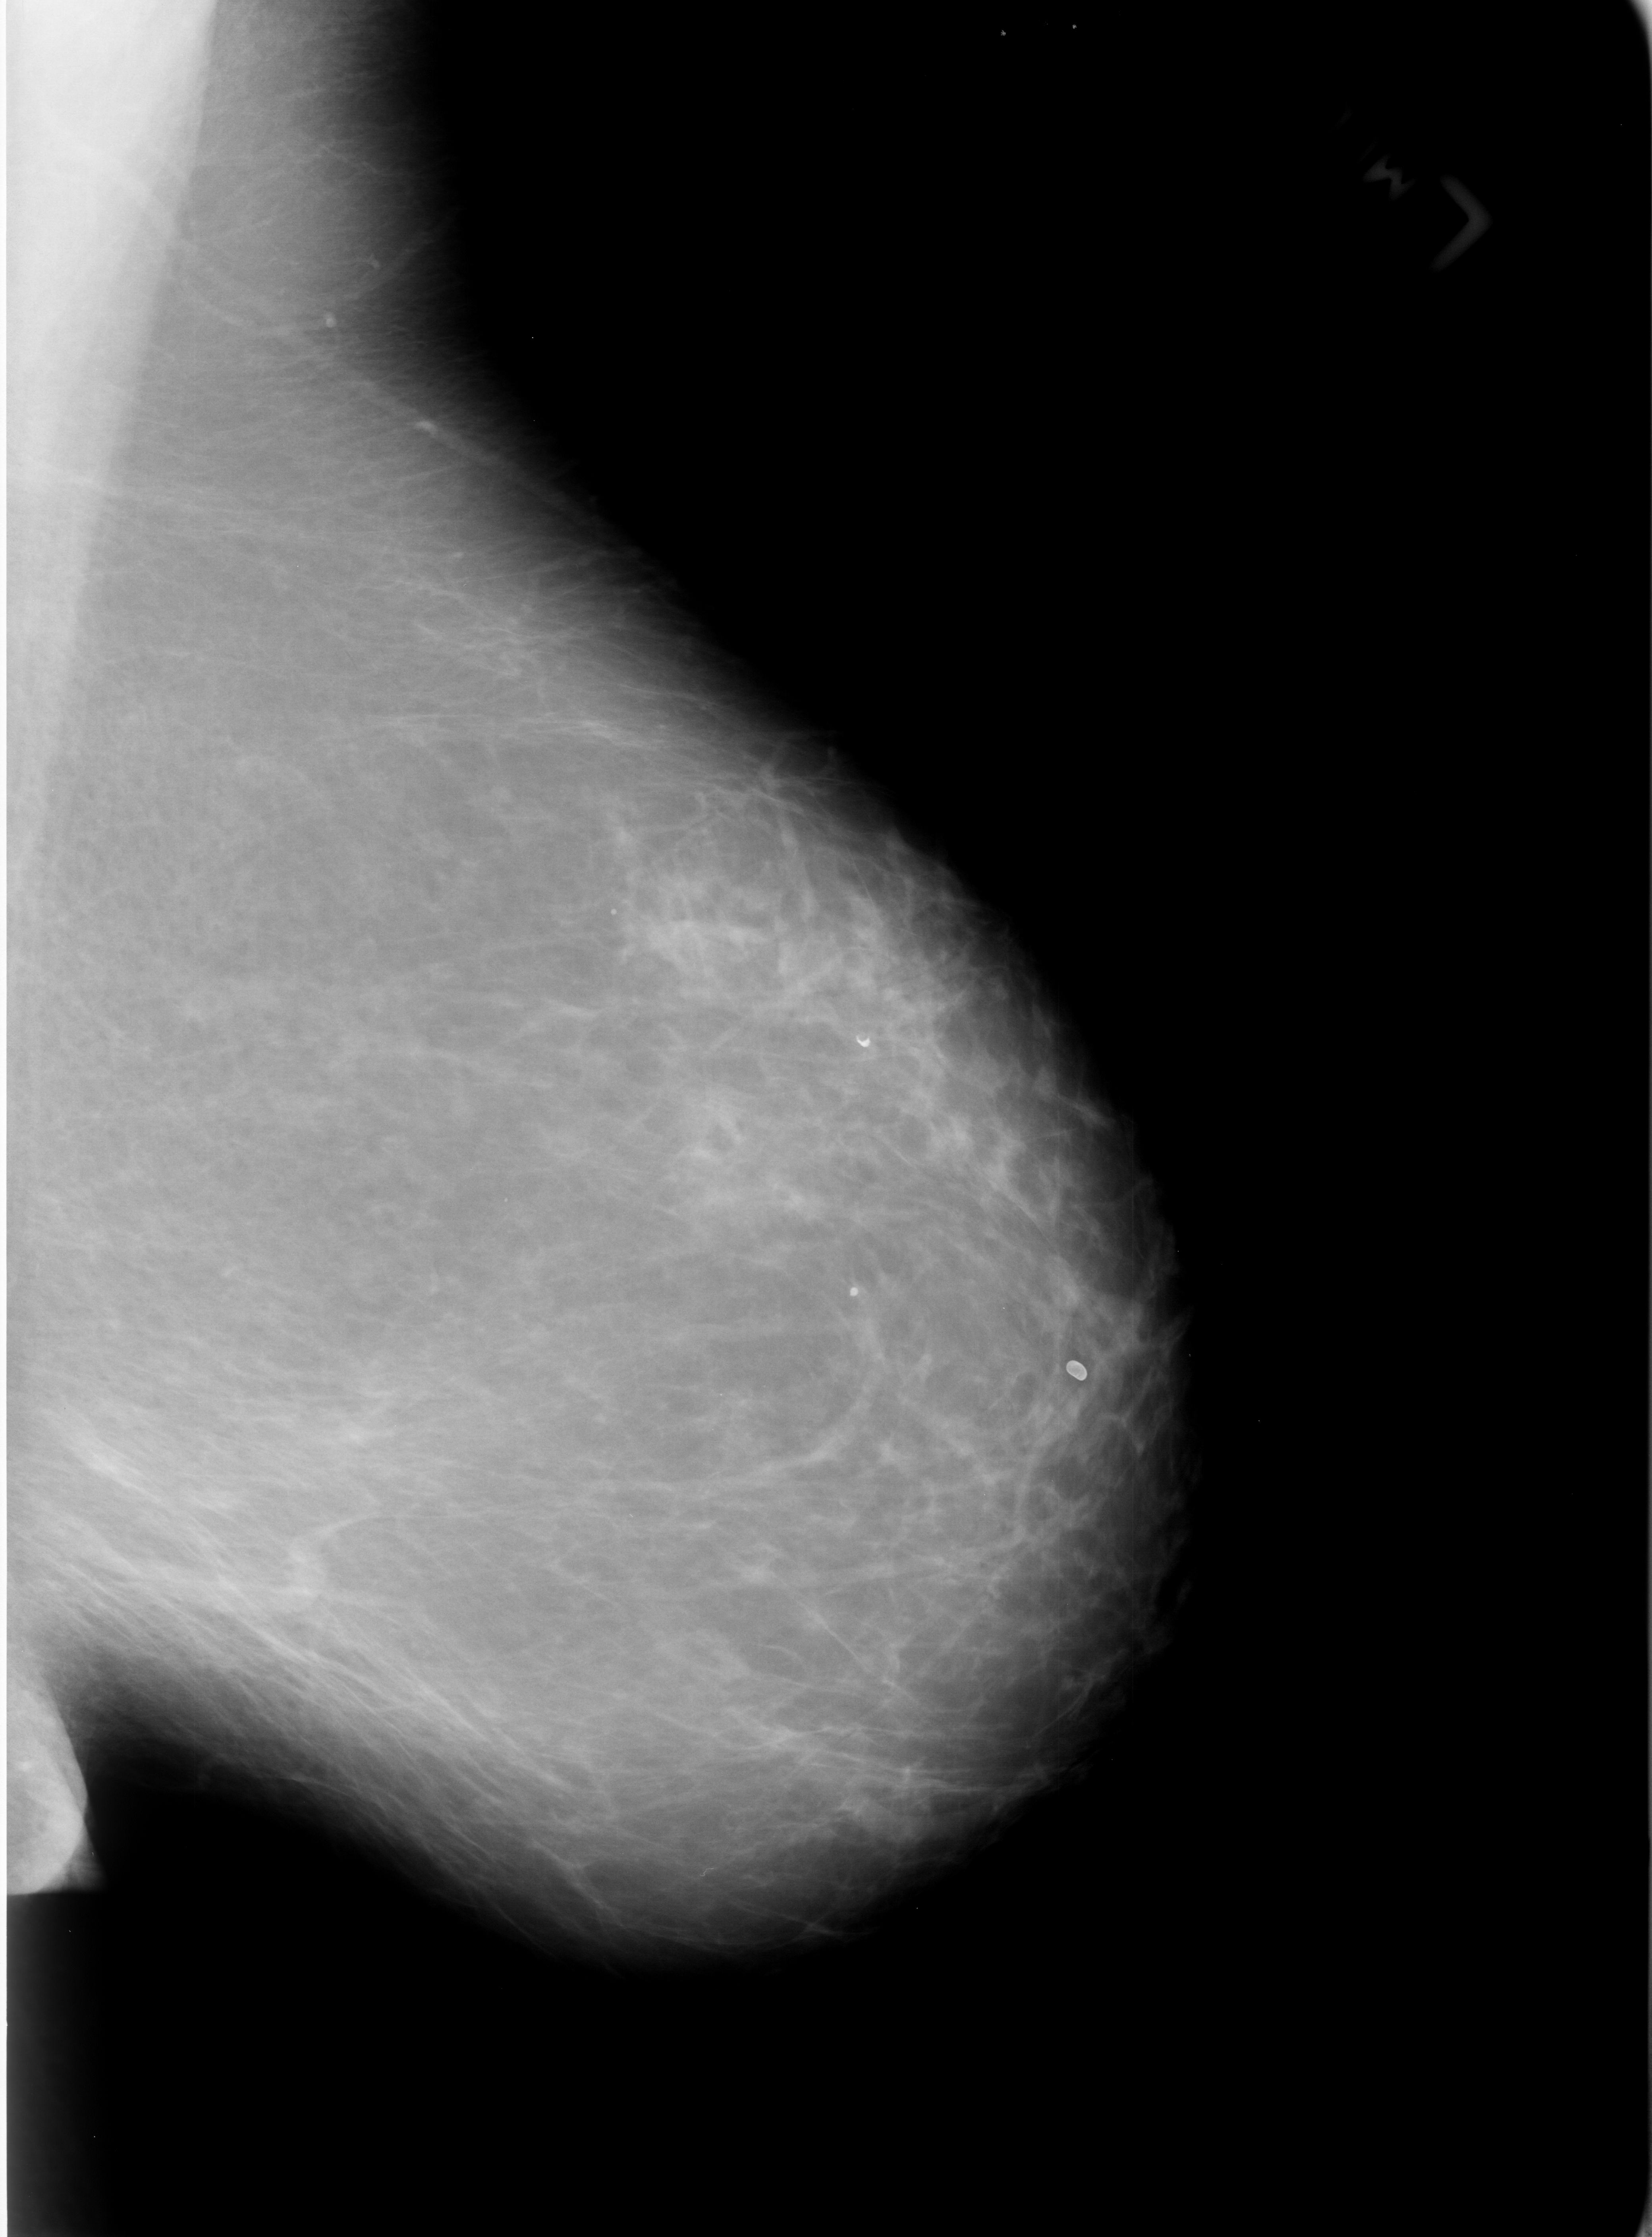
Digitized screen-film mammogram; left breast; MLO view; BI-RADS breast density category 2 (scale 1–4); 1652 × 2237 image matrix.
Marked abnormalities (boxes around the expert regions of interest):
- Finding 1 of 3: calcifications, morphology lucent center; BI-RADS assessment category 2; outcome (as recorded, no biopsy): benign without callback (not worked up further): bounding box <822,1264,890,1326> (left, top, right, bottom; pixels)
- Finding 2 of 3: calcifications, morphology lucent center; BI-RADS assessment category 2; benign; no additional work-up was recommended (outcome (as recorded, no biopsy): benign without callback): <835,1016,906,1075>
- Finding 3 of 3: calcifications, morphology lucent center; BI-RADS assessment category 2; subtlety rating 5 on a 1 (subtle) to 5 (obvious) scale; benign; no additional work-up was recommended (outcome (as recorded, no biopsy): benign without callback): <1042,1337,1097,1393>